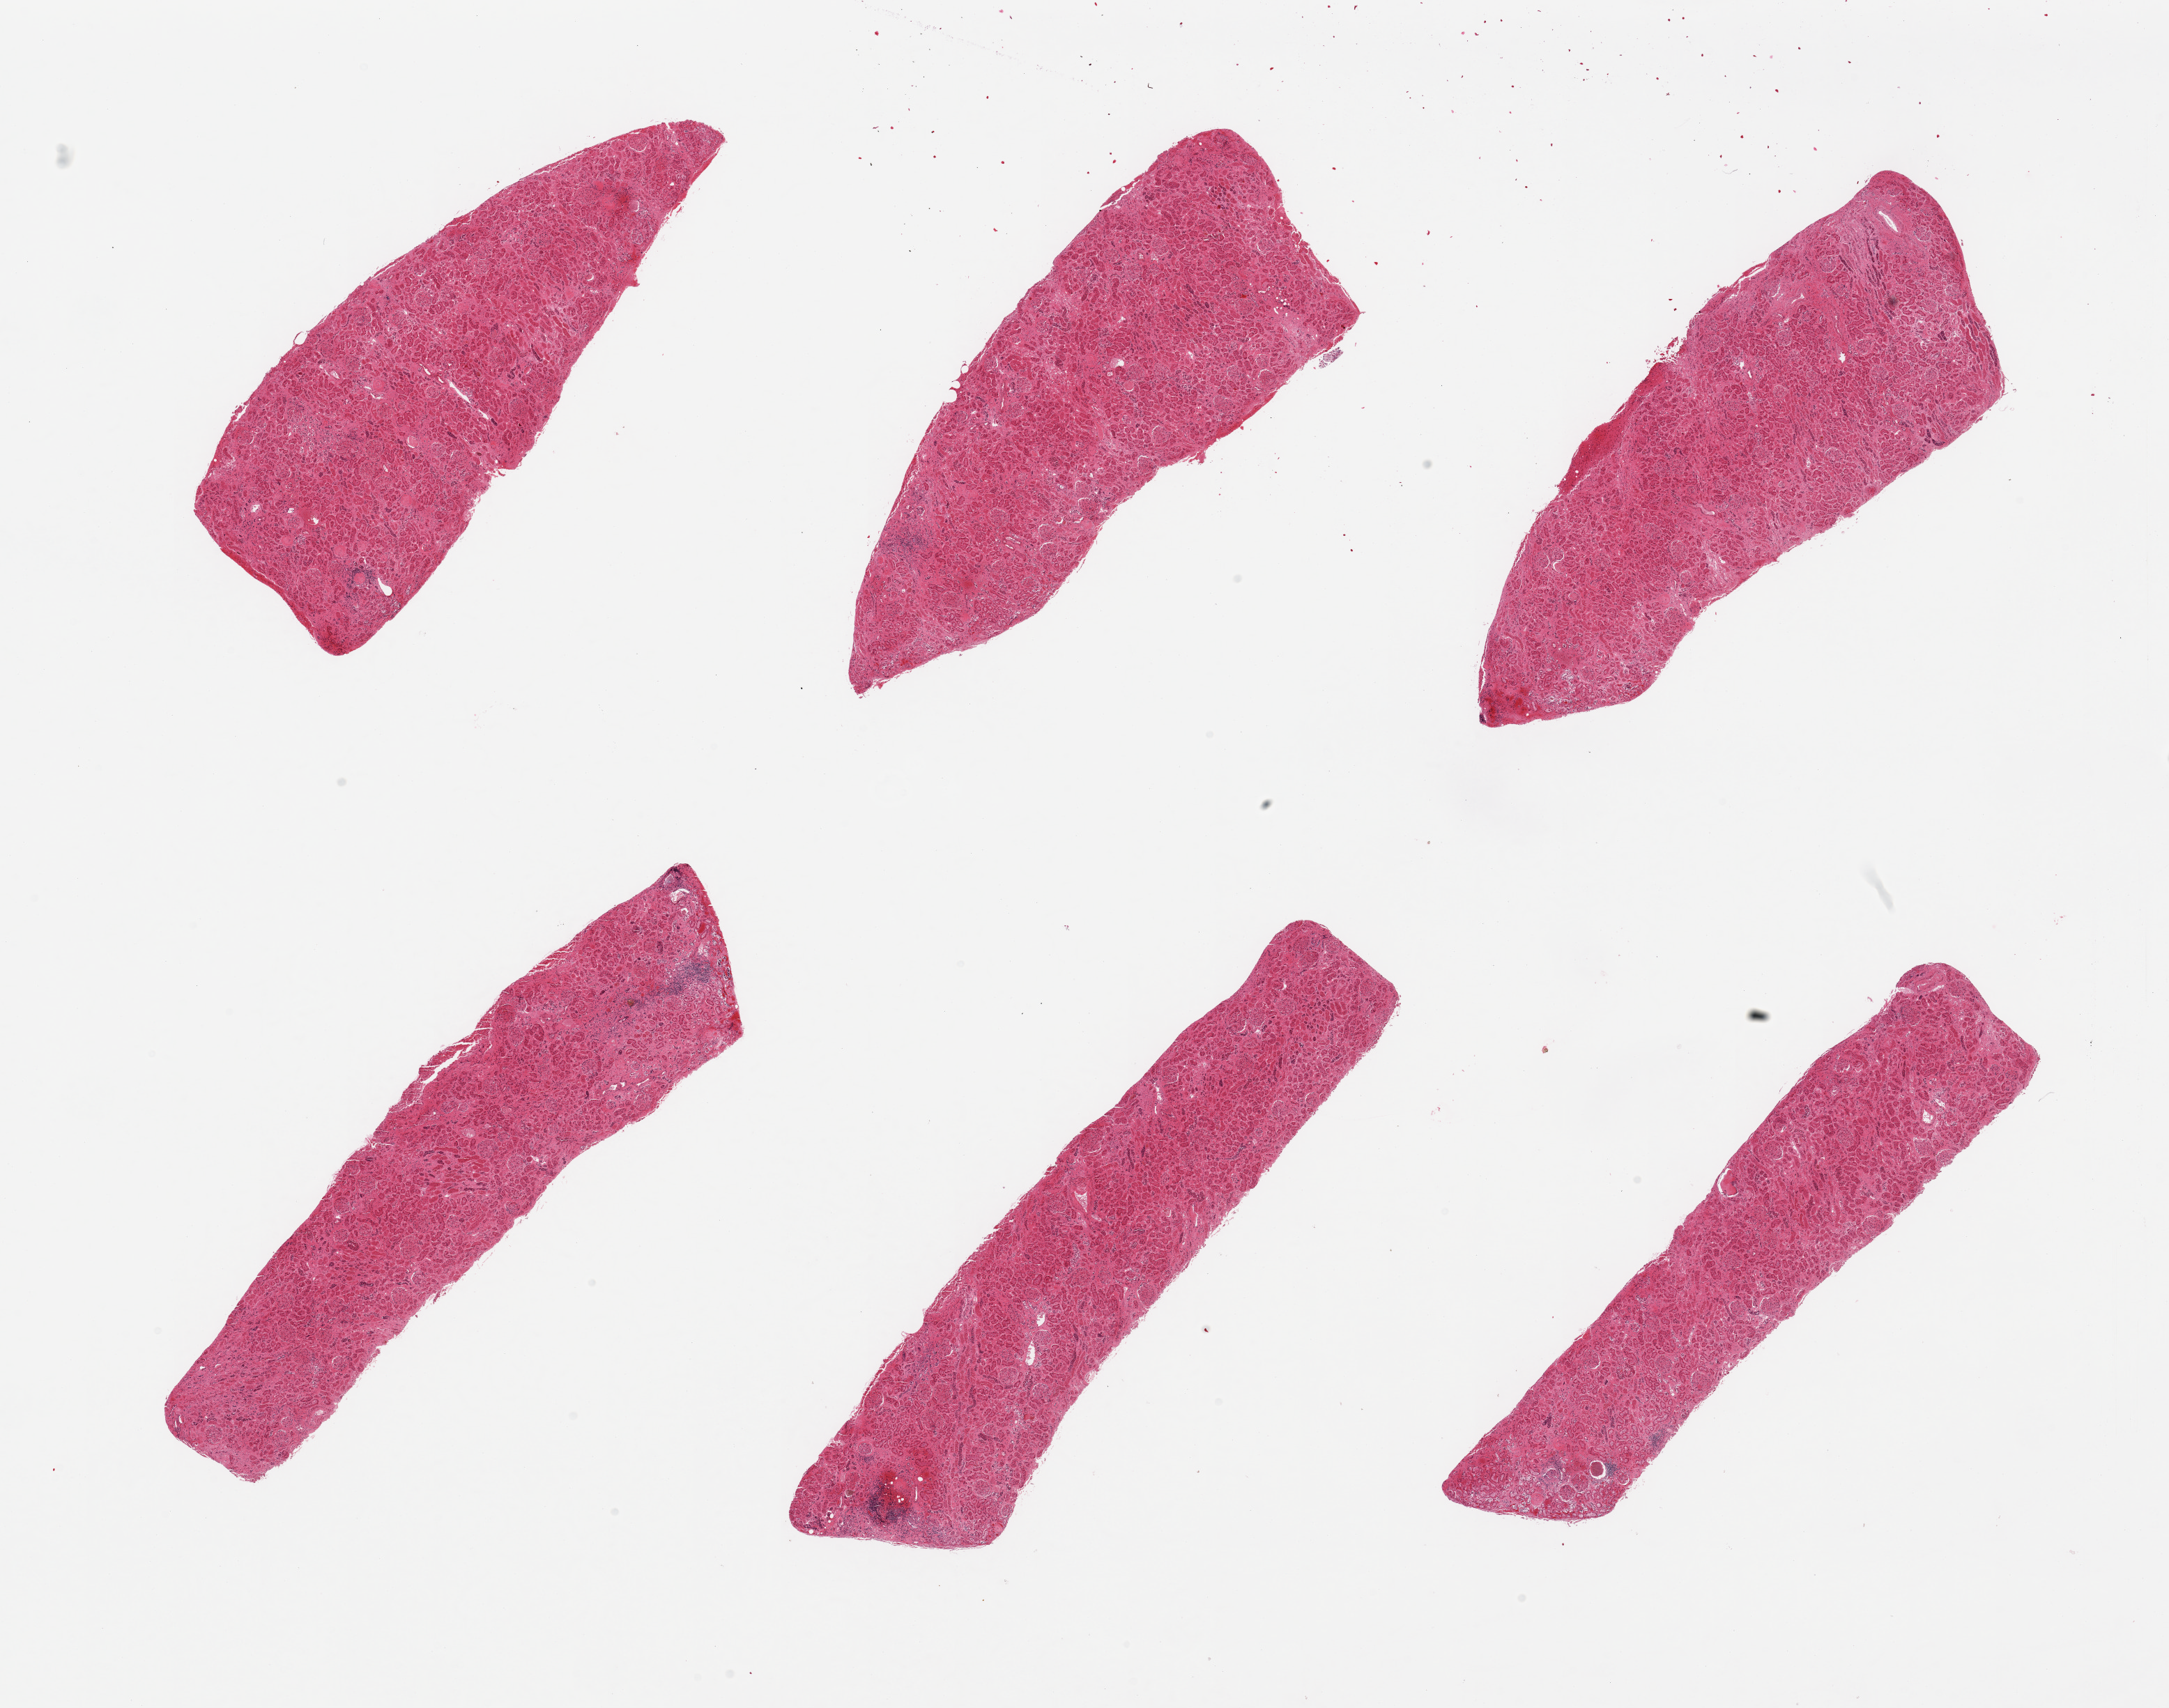
Haematoxylin and eosin whole-slide image — low-resolution overview of the scanned area, about 24.6 x 19.4 mm, PAXgene-fixed paraffin-embedded (PFPE) section, target tissue: renal cortex, donor tissue sample. Male donor.
Reviewer comment on this tissue sample: 6 pieces; scattered sclerotic glomeruli and lymphoid foci.